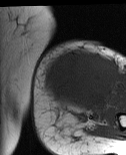
MRI of an extremity soft-tissue mass, one axial slice. Slice 23 of 86 in the series (ordered by position). MR volume resampled by the dataset authors to the PET/CT grid (not the native acquisition matrix). 3.27 mm slice thickness. 126 × 155 image matrix, field of view 123 × 151 mm. Female patient. Case-level facts recorded for this patient, not image findings: histological type: pleiomorphic leiomyosarcoma; grade: high; site of the primary tumour: left biceps.
Structures marked on this image (expert contour drawn on MRI and transferred to this co-registered scan by the dataset authors):
- gross tumour volume including surrounding oedema: bounding box (x1, y1, x2, y2) in pixels: (43, 51, 117, 112)
- gross tumour volume (mass): (43, 51, 117, 109)